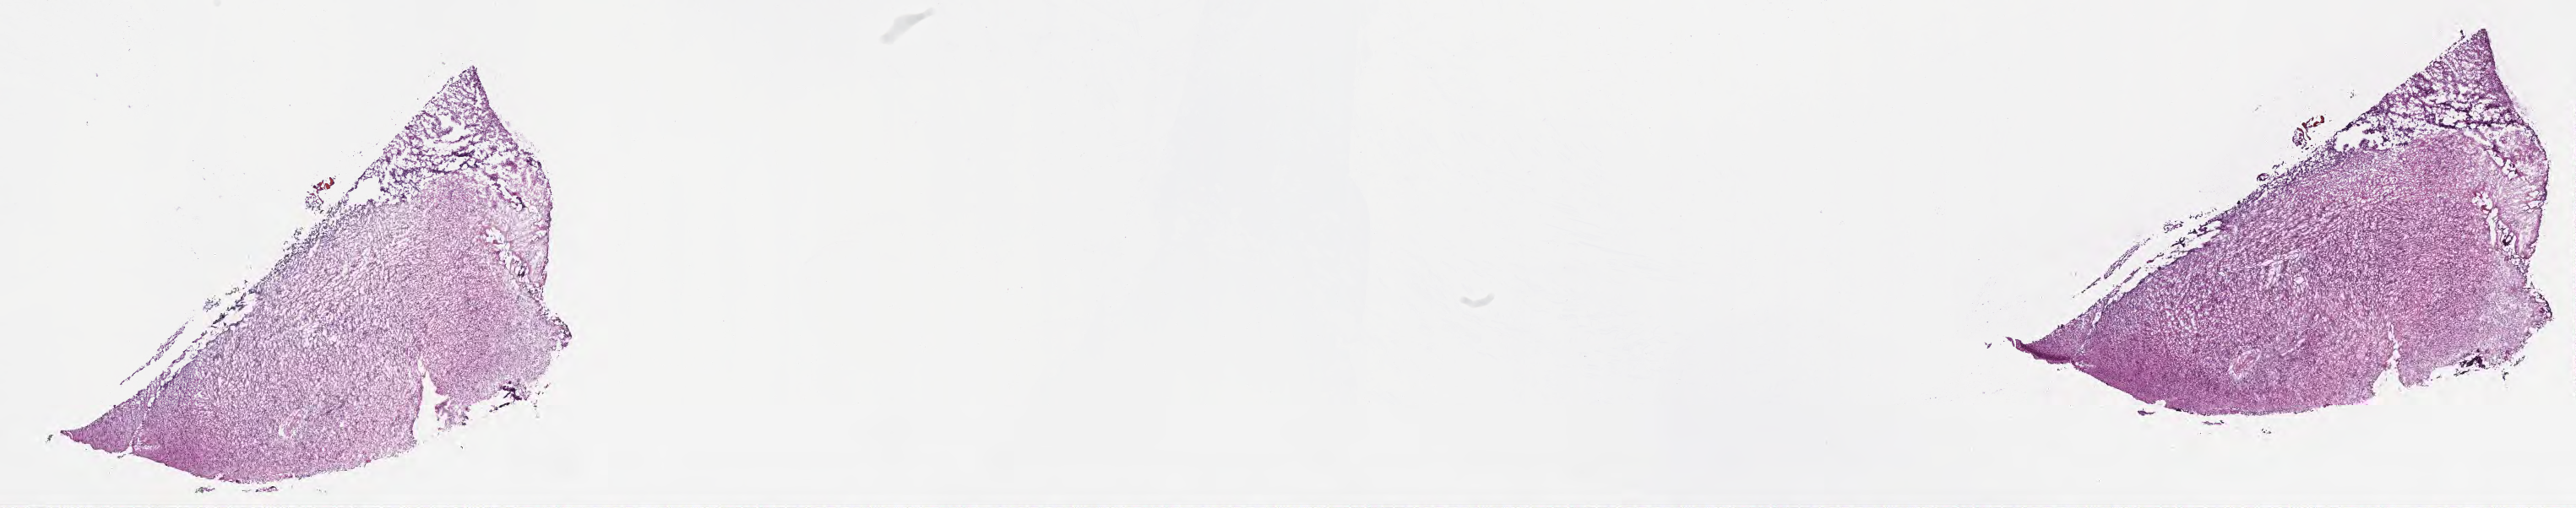
Hematoxylin and eosin (H&E) whole-slide image of tumor tissue from the cerebral ventricle, whole scanned area (about 24.7 x 4.9 mm) shown as a low-resolution overview, cryosection (OCT / tissue freezing medium). Patient male; age 93 months (7 years 9 months).
* diagnosis (ICD-O-3 morphology term): Medulloblastoma, NOS